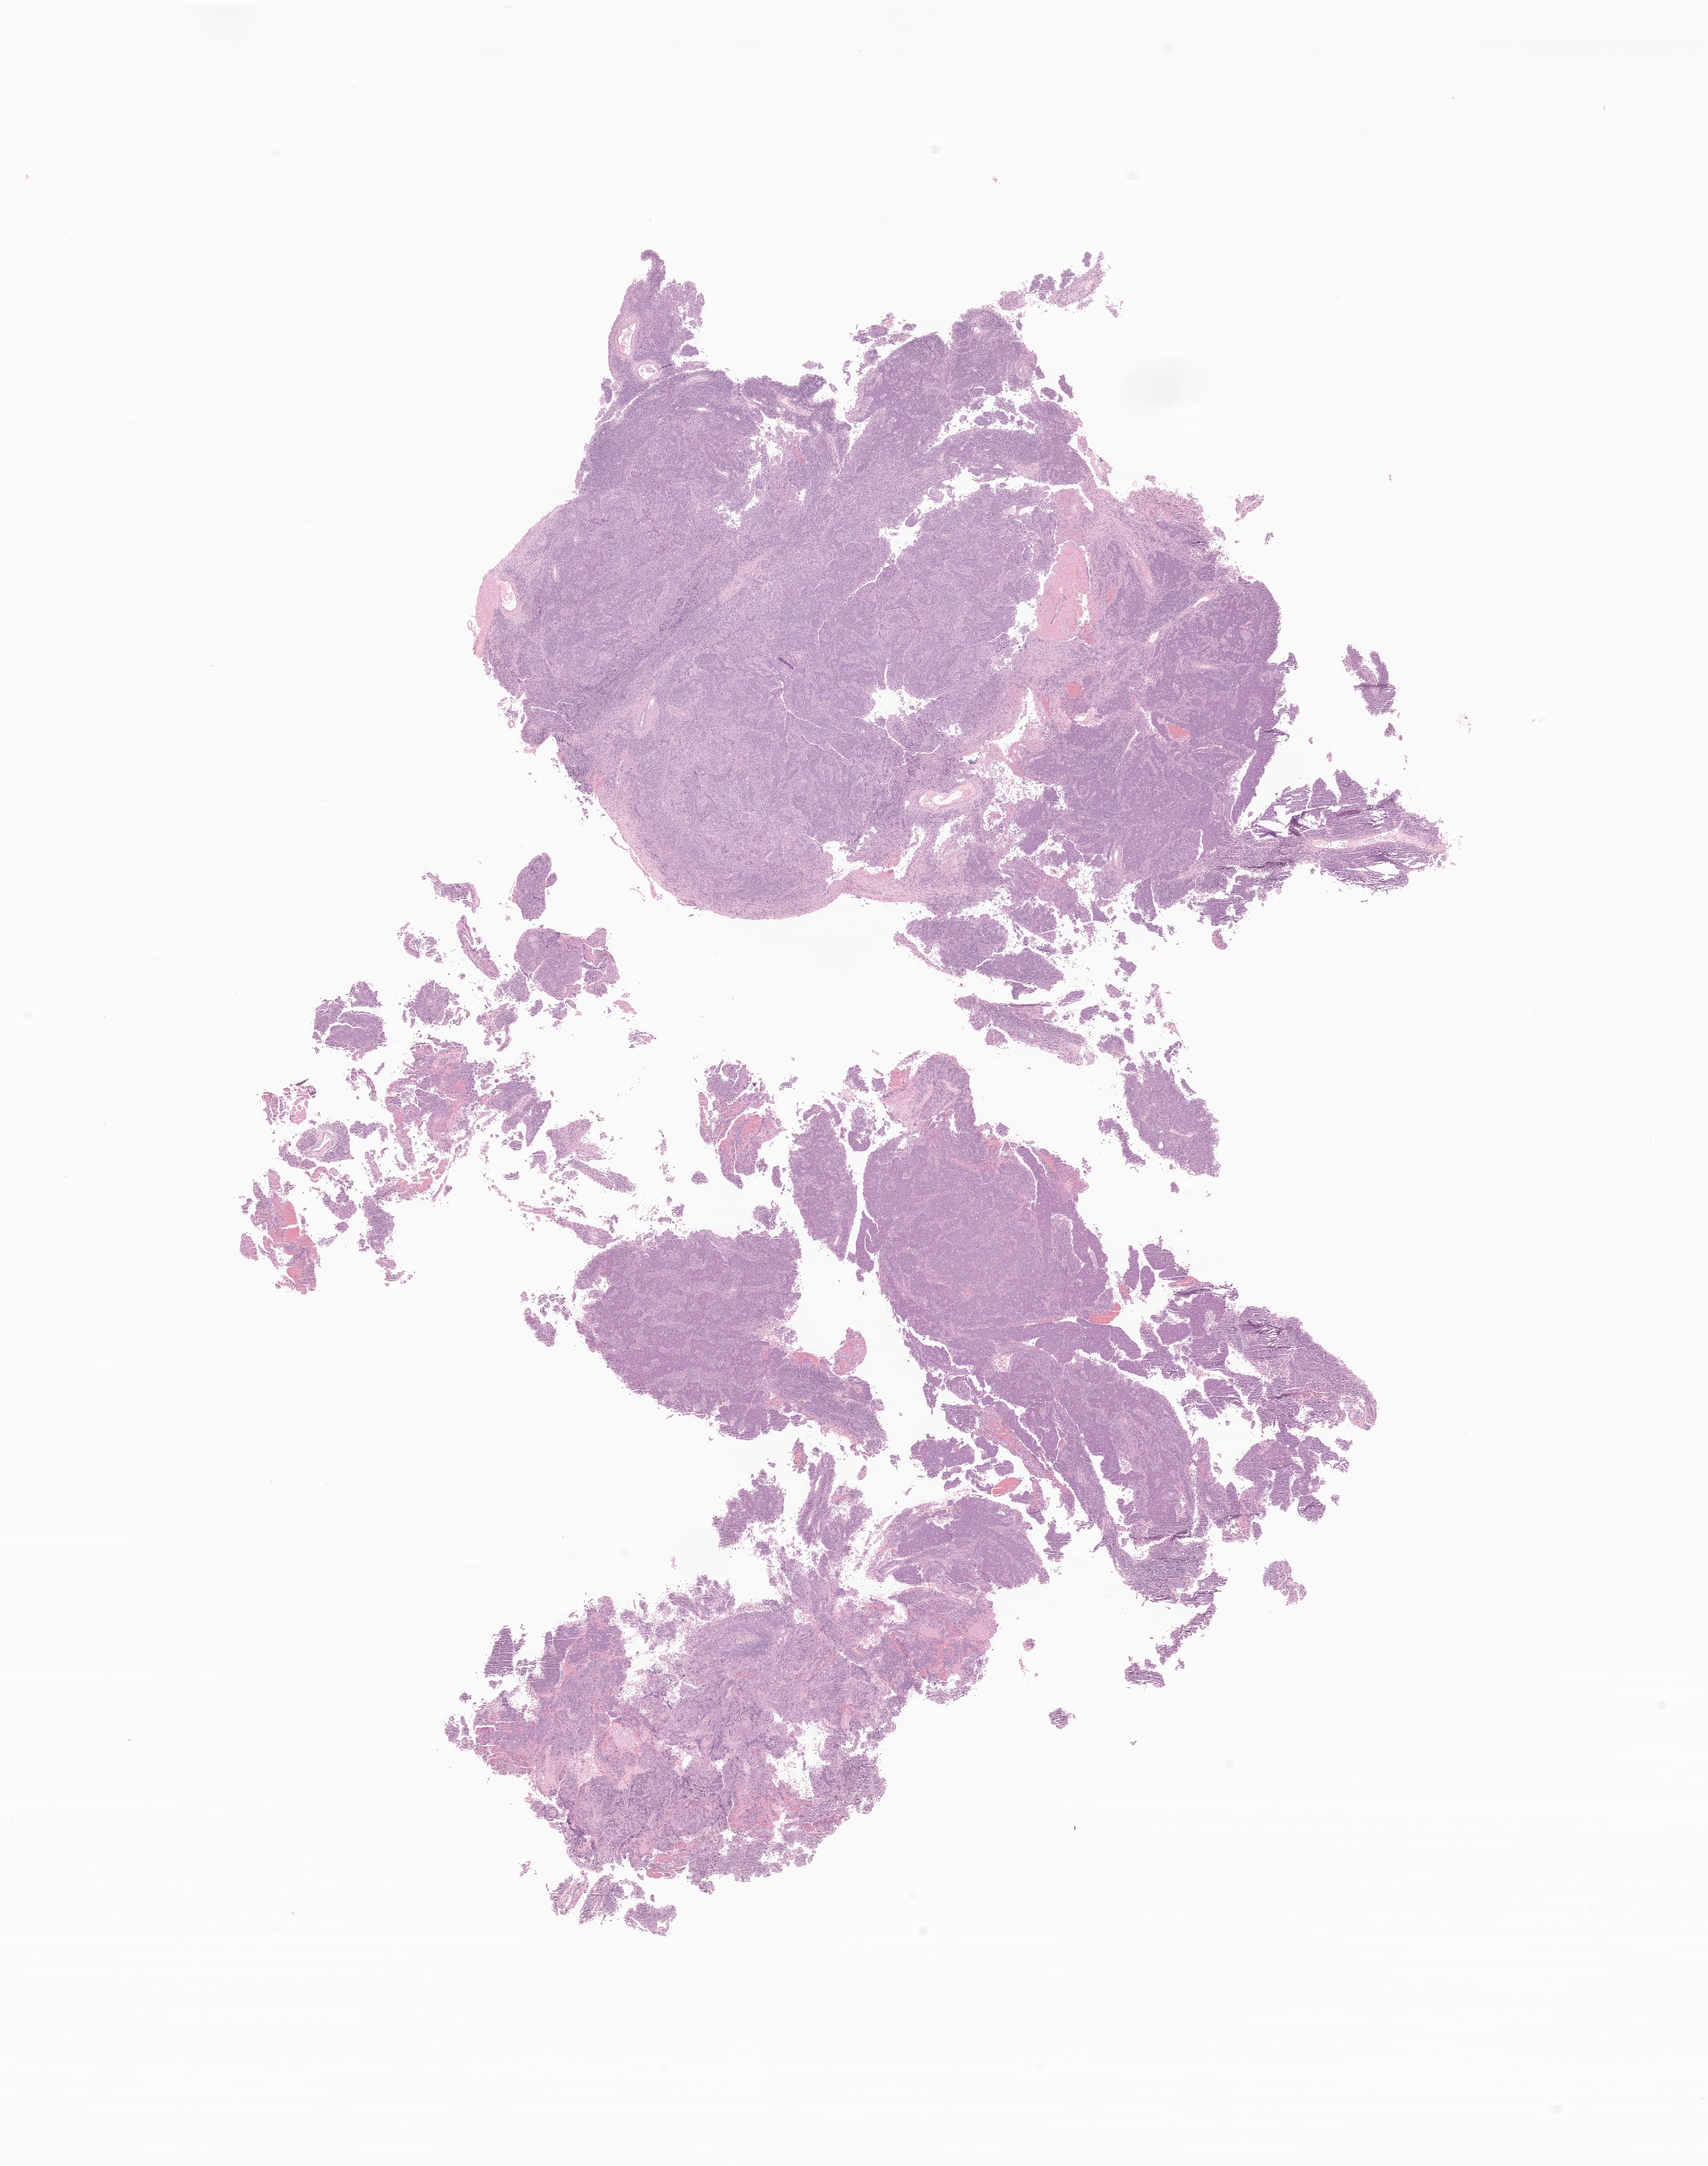
Whole-slide image, hematoxylin and eosin (H&E) stain of tumor tissue from the nasopharynx — a low-resolution overview of the entire scanned area, about 13.8 x 17.5 mm, formalin-fixed, paraffin-embedded (FFPE) tissue. Patient female; age 214 months (17 years 10 months).
Recorded diagnosis: Squamous cell carcinoma, NOS.